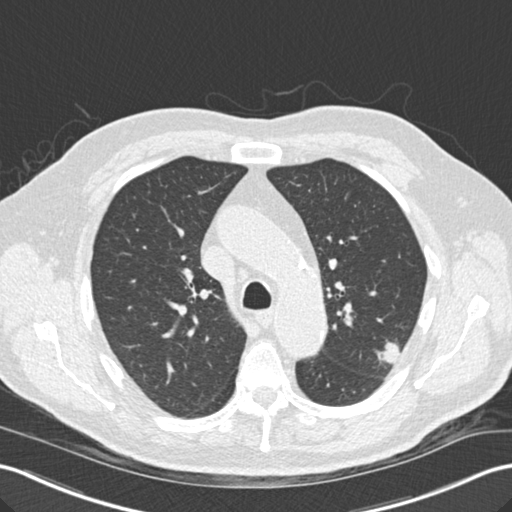
Chest CT (low-dose screening protocol), one axial image; third screening round (two years after baseline); lung window (W 1500 / L -600 HU); 2 mm slice thickness; standard (soft-tissue) reconstruction kernel (B30f); slice 52 of 157 in the series; 512 × 512 image matrix, field of view 354 × 354 mm. Male, age 67 years at enrolment. Former smoker at enrolment.
• Expert reader's lesion annotation, bounding box [x1, y1, x2, y2] px = [365, 333, 410, 373].
• The screening reader recorded 2 non-calcified nodules or masses ≥4 mm on this exam; which of them this box marks is not recorded.
• Participant outcome: lung cancer diagnosed 55 days after this screen — squamous cell carcinoma, large cell, nonkeratinizing, NOS, left upper lobe, moderately differentiated (G2), stage IA (AJCC 6th edition), 15 mm at pathology.